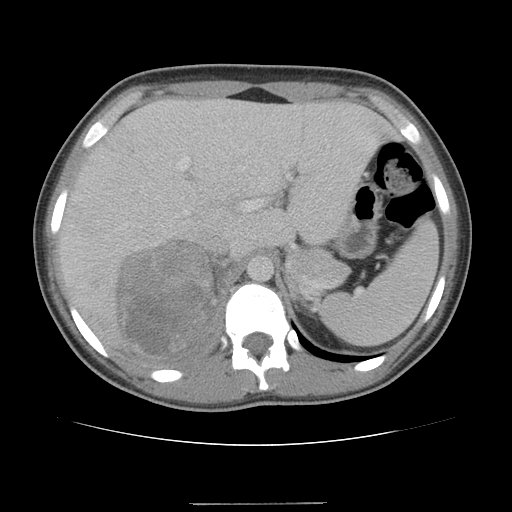
Contrast-enhanced abdominal CT, one axial slice. Position 77 of 100 along the scan axis. 120 kVp. Intravenous contrast given. Soft-tissue window (W 400 / L 40 HU). 5 mm slice thickness. 512 × 512 image matrix. Female patient, age 21 years. Case-level facts recorded for this patient, not image findings: diagnosis: adrenocortical carcinoma; tumour side: right adrenal; tumour size at pathology: 15.5 cm; Ki-67 index: 26 %; stage (as recorded): 3.
Structures marked on this image (semi-automatically segmented with operator editing):
- mass: bounding box [x1, y1, x2, y2] px = [118, 241, 215, 358]